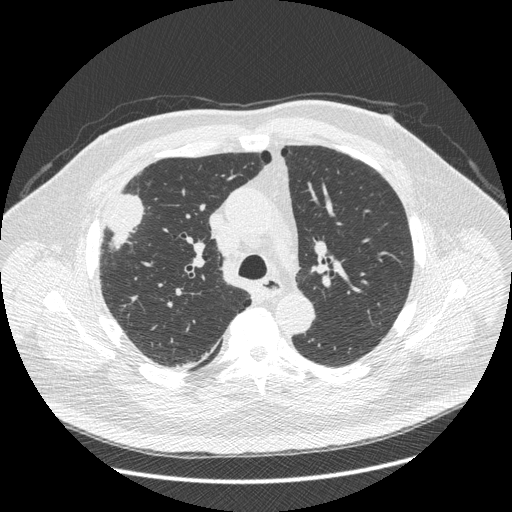
Low-dose screening chest CT, one axial slice; position 287 of 426 along the scan axis; 120 kVp; lung window (W 1500 / L -600 HU); 1.25 mm slice thickness; 512 × 512 image matrix, field of view 400 × 400 mm.
Structures marked on this image (manually delineated by an expert):
- lesion 1 (tumor, upper lobe of right lung): bounding box (x1, y1, x2, y2) in pixels: (106, 194, 144, 248)